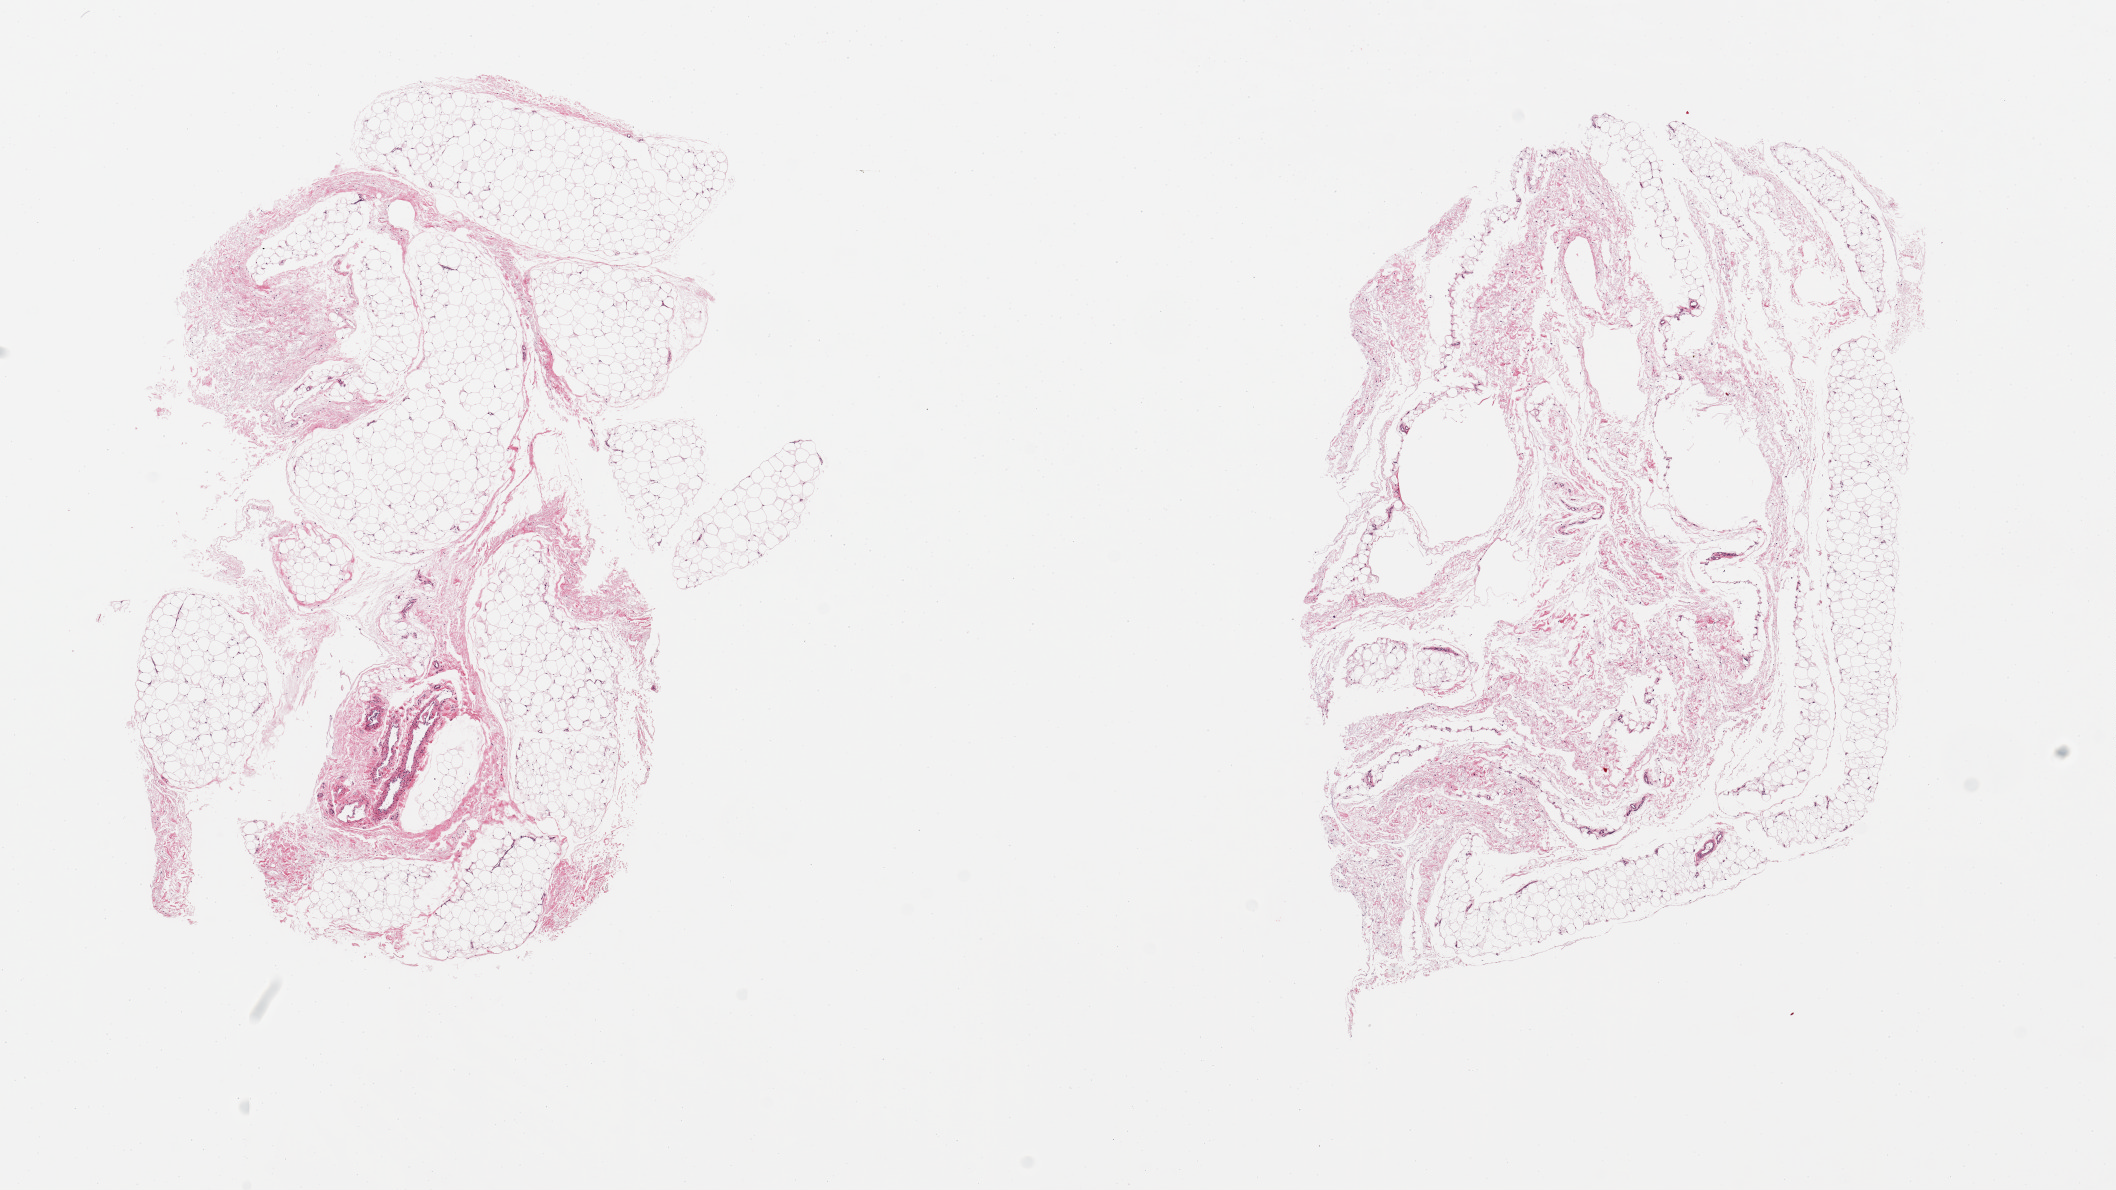
Whole-slide image, haematoxylin and eosin stain — whole scanned area (about 16.7 x 9.4 mm) shown as a low-resolution overview; PAXgene-fixed paraffin-embedded (PFPE) section; target tissue: adipose tissue; donor tissue sample. Donor sex: male.
Pathologist's review note for this sample: 2 pieces, 10-20% fascia/vascular elements.